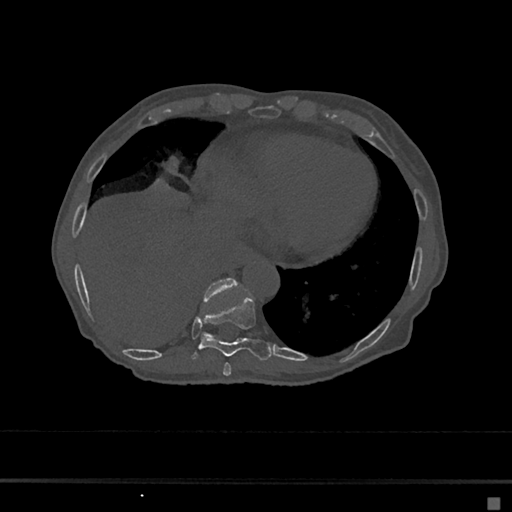
CT including the spine, one axial slice. Reconstruction kernel Br40s/3. 120 kVp. Bone window (W 1800 / L 400 HU). 0.5 mm slice thickness. 512 × 512 image matrix, field of view 360 × 360 mm. Patient: female, 68 years. From the clinical record (not read from this slice): primary cancer: renal.
Annotated regions visible in this slice (semi-automatic segmentation, software-assisted and operator-edited):
- T10 vertebra: bounding box [x1, y1, x2, y2] px = [203, 279, 240, 338]
- T8 vertebra: [223, 363, 231, 376]
- T9 vertebra: [191, 295, 273, 360]